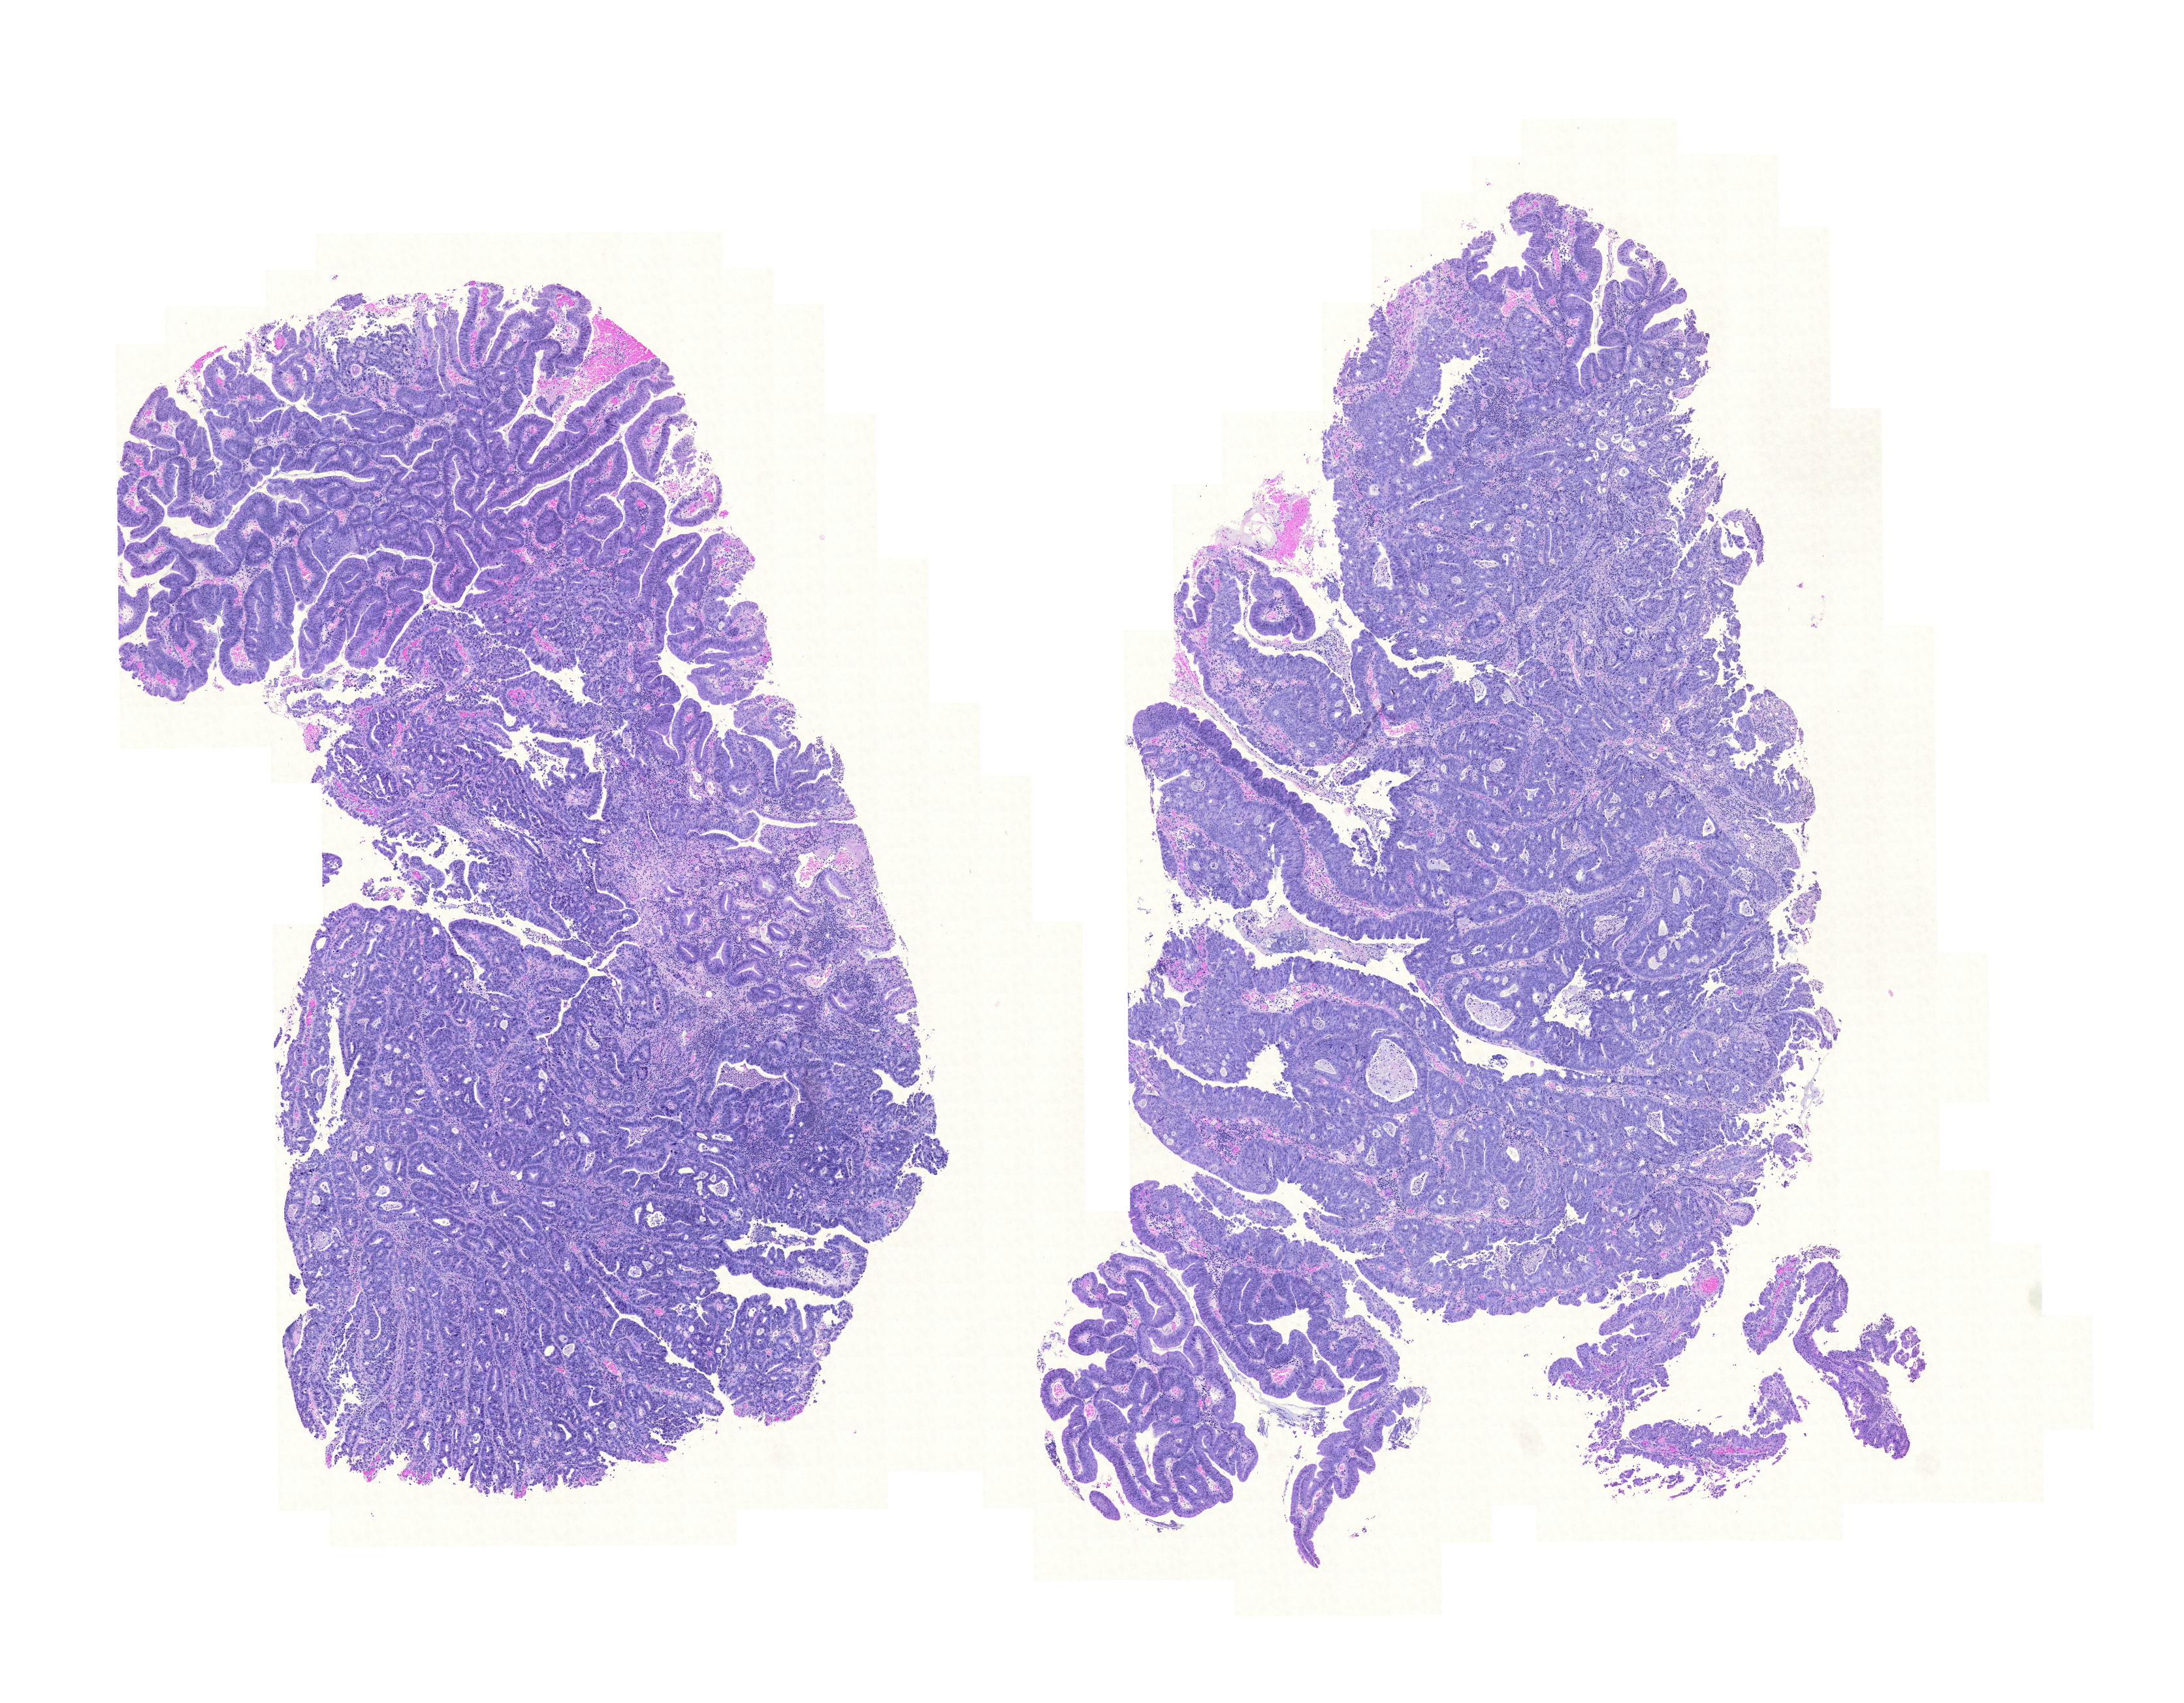
Whole-slide histology image, H&E — shown as a low-resolution overview of the whole scanned area (about 12.4 x 9.7 mm). FFPE section. Primary tumour sample from the colon. Patient: male, age at initial diagnosis 50 years.
• AJCC pathologic stage: IIIB (6th edition)
• pathologic diagnosis: Adenocarcinoma, NOS (ascending colon)